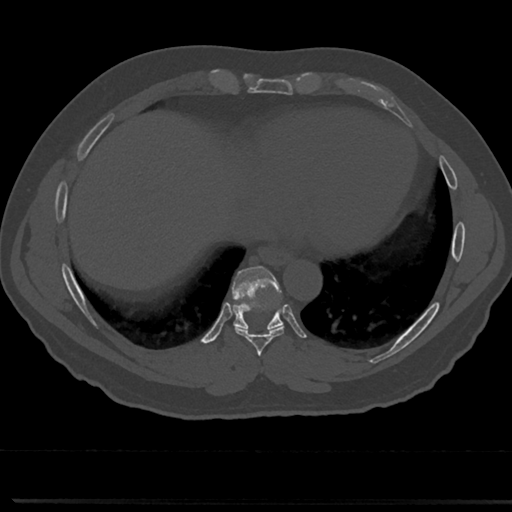
CT including the spine, one axial slice; slice 334 of 817 in the series (ordered by position); 120 kVp; bone window (W 1800 / L 400 HU); 0.5 mm slice thickness; 512 × 512 image matrix, field of view 355 × 355 mm. Male patient, age 61 years. From the clinical record (not read from this slice): primary cancer: prostate.
Outlined on this slice (semi-automatic segmentation, software-assisted and operator-edited):
- T7 vertebra: bounding box [x1, y1, x2, y2] px = [259, 346, 266, 377]
- T8 vertebra: [211, 271, 309, 356]